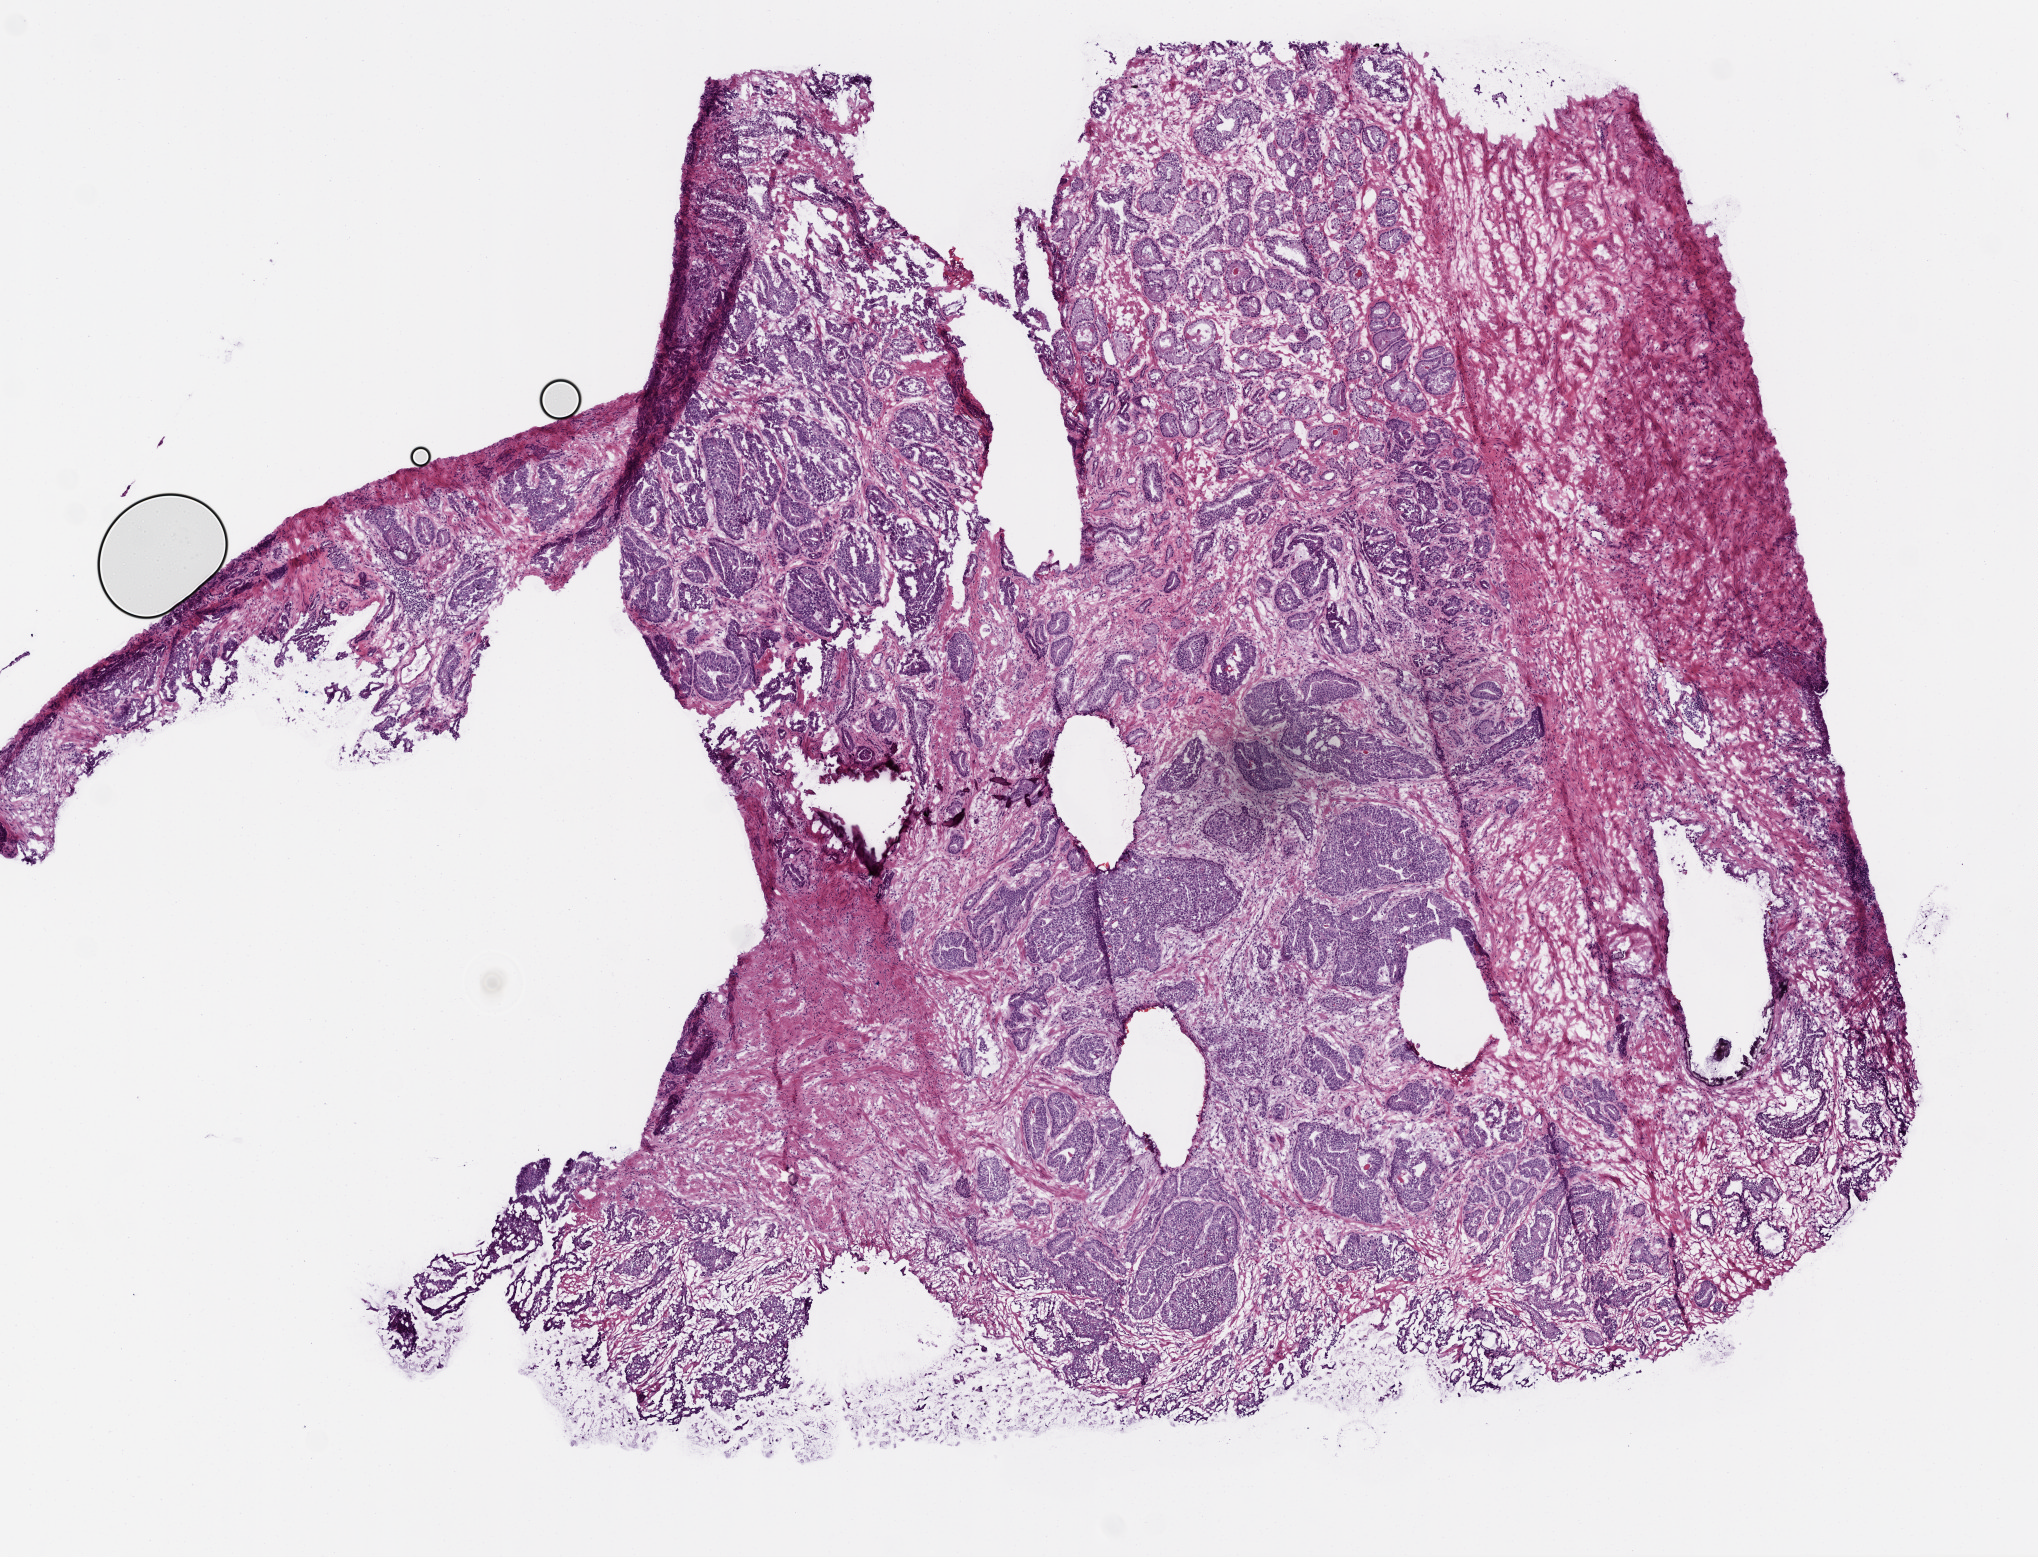
Whole-slide histology image, Hematoxylin and eosin (H&E) stained, whole scanned area (about 8.2 x 6.3 mm, from a 20x scan) shown as a low-resolution overview. Frozen section from the top of the tissue portion. Primary tumour sample from the prostate. Patient: male, age at initial diagnosis 57 years. Gleason score: 8 (4+4). Composition of this section per pathologist review: tumour cells 70%, tumour nuclei 70%, normal cells 20%, stromal cells 10%, necrosis 0%.
Diagnosis: Acinar cell carcinoma. Lymph nodes positive (case pathology): 0 of 8 examined.